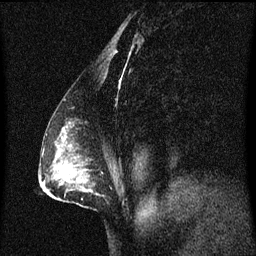
Breast MRI (dynamic contrast-enhanced), one sagittal slice; dynamic contrast-enhanced series, image 2 of 3 at this slice position (ordered by acquisition); 1.5 T; TE 4.2 ms, TR 8.4 ms; 256 × 256 image matrix. Patient: female, 40 years. From the clinical record (not read from this slice): setting: breast cancer imaged before/during neoadjuvant chemotherapy; receptor status: triple-negative.
Outlined on this slice (semi-automatically segmented with operator editing):
- analysis volume of interest (the breast-tissue region the enhancement analysis was run in; not a lesion): box from (x=58, y=120) to (x=119, y=209) px
- tumour enhancement mask (voxels above the 70 % enhancement threshold inside the analysis volume of interest): (x=62, y=130)–(x=67, y=137)